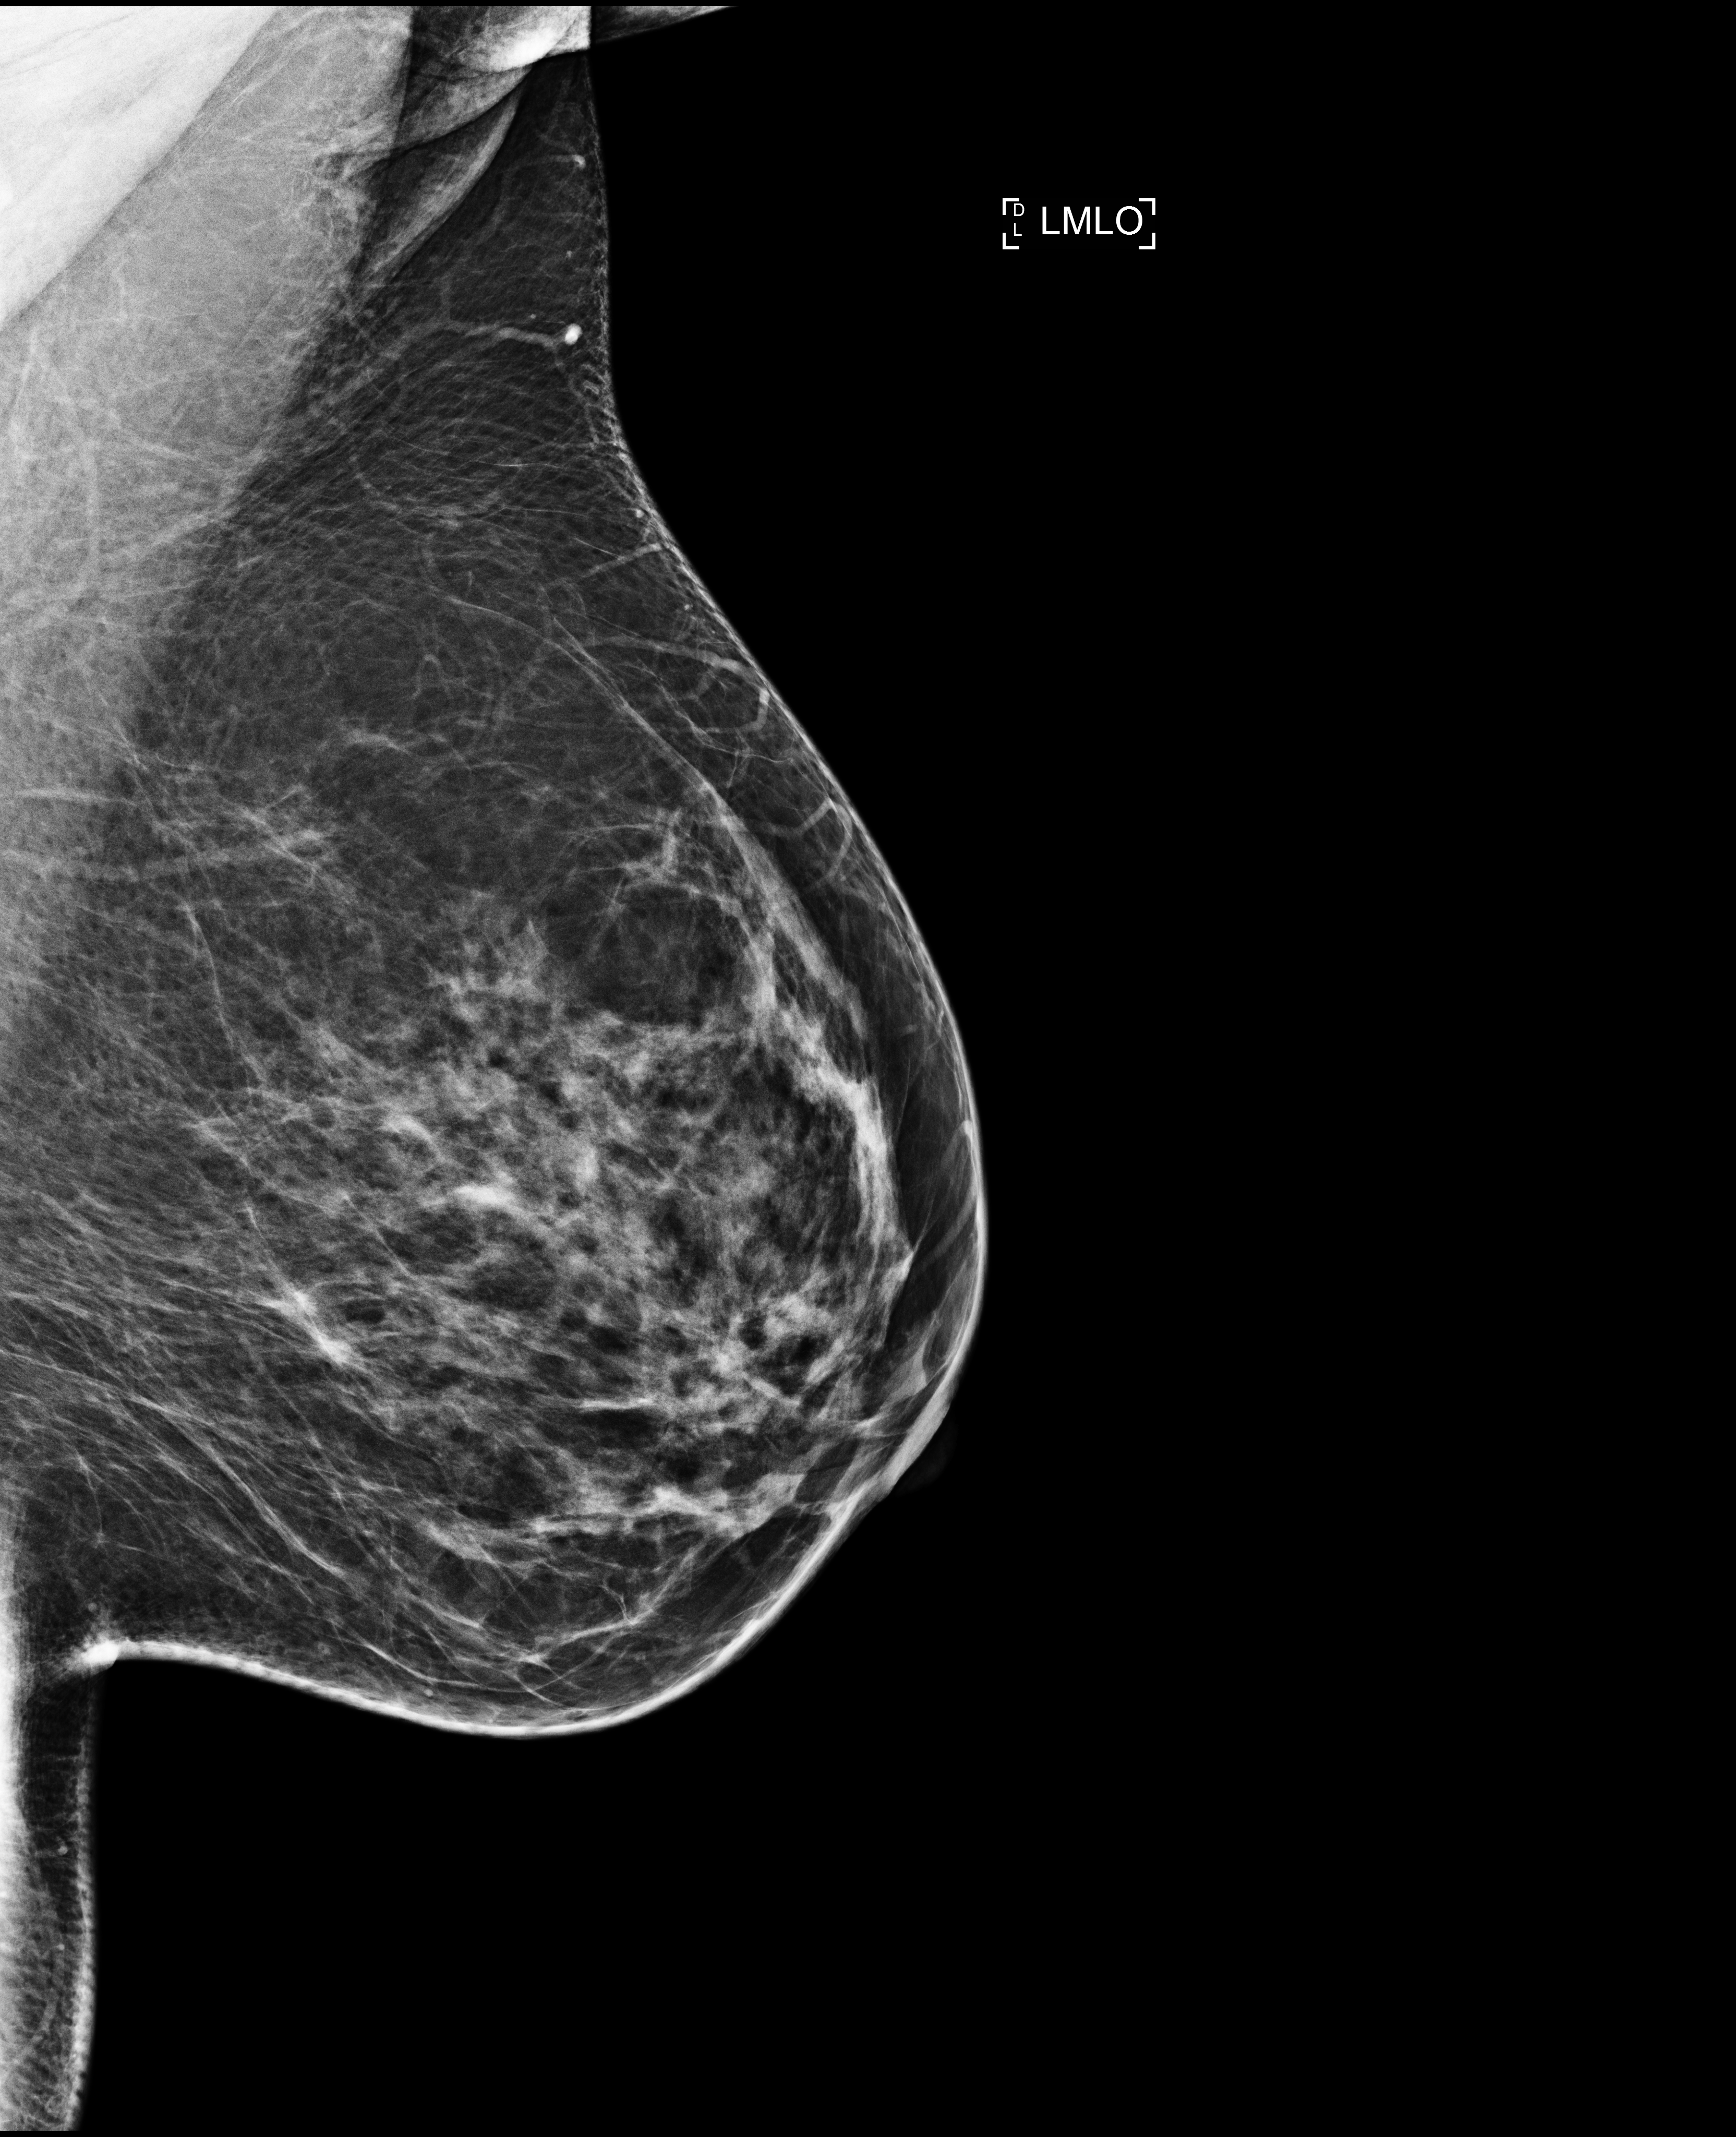
Annual screening mammography examination, compressed breast thickness 69 mm. Female patient, age 47 years.
Image type: full-field digital mammogram. Breast: left. Projection: mediolateral oblique (MLO) view.